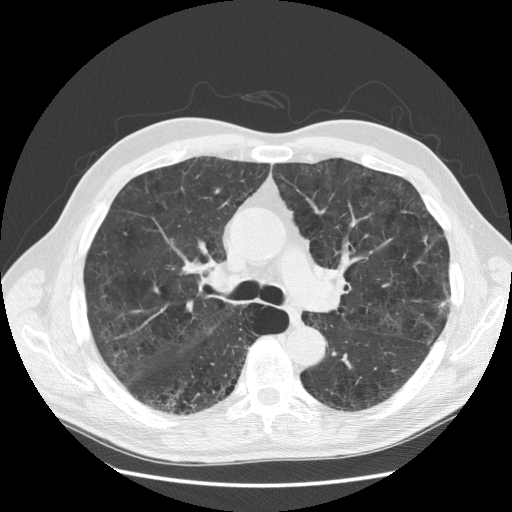
Chest CT (low-dose screening protocol), one axial image. Third screening round (two years after baseline). Lung window (W 1500 / L -600 HU). Standard (soft-tissue) reconstruction kernel (STANDARD). Slice 67 of 163 in the series. Male, age 58 years at enrolment. Current smoker at enrolment.
Expert reader's lesion annotation, bounding box (x1, y1, x2, y2) in pixels: (409, 224, 443, 257). The exam's reader record, not a measurement of the box and not confirmed to be the same lesion: non-calcified nodule or mass ≥4 mm, left upper lobe, 9 × 8 mm, poorly defined margins, soft tissue attenuation, pre-existing on the prior screen: no. Later outcome: lung cancer diagnosed 53 days after this screen — adenocarcinoma, NOS, left upper lobe, stage IA (AJCC 6th edition), 9 mm at pathology.